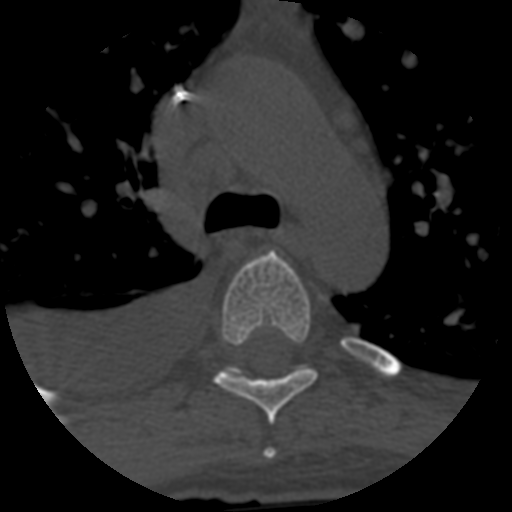
CT including the spine, one axial slice; slice 452 of 708 in the series (ordered by position); 120 kVp; one of 3 acquisitions stored at this slice position; bone window (W 1800 / L 400 HU); 512 × 512 image matrix, field of view 160 × 160 mm. Patient age 55 years. Case-level facts recorded for this patient, not image findings: primary cancer: colon; vertebrae with lytic lesions (as recorded): T12, L1, L5.
Structures marked on this image (semi-automatic segmentation, software-assisted and operator-edited):
- T4 vertebra: bounding box [x1, y1, x2, y2] px = [263, 447, 277, 460]
- T5 vertebra: [214, 252, 318, 425]
- T6 vertebra: [229, 365, 312, 374]